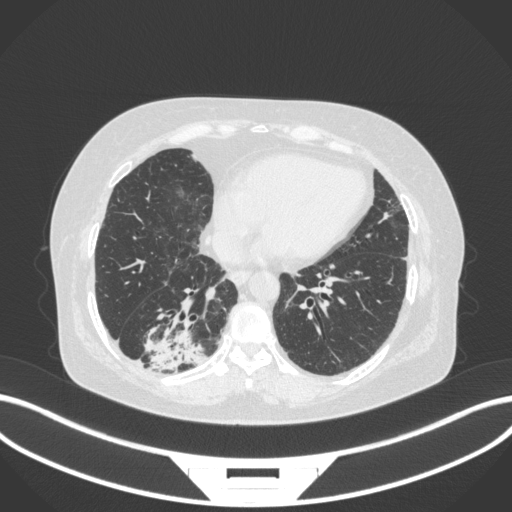
Chest CT, one axial slice; position 75 of 303 along the scan axis; reconstruction kernel B31f; 120 kVp; lung window (W 1500 / L -600 HU); 1 mm slice thickness; 512 × 512 image matrix. Patient: female, 65 years. Case-level facts recorded for this patient, not image findings: clinical TNM (as recorded): T2b N1 M0; histopathological grade: G1.
Structures marked on this image (rectangle marked by the reading radiologist):
- lung tumour (recorded histology: adenocarcinoma): bounding box <143,307,209,373> (left, top, right, bottom; pixels)